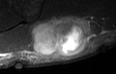
MRI of an extremity soft-tissue mass, one axial slice. Position 19 of 36 along the scan axis. STIR. MR volume resampled by the dataset authors to the PET/CT grid (not the native acquisition matrix). 3.27 mm slice thickness. 116 × 74 image matrix, field of view 113 × 72 mm. Male patient. Case-level facts recorded for this patient, not image findings: histological type: pleiomorphic leiomyosarcoma; grade: high; site of the primary tumour: left buttock.
Outlined on this slice (expert contour drawn on MRI and transferred to this co-registered scan by the dataset authors):
- gross tumour volume including surrounding oedema: box from (x=28, y=17) to (x=86, y=57) px
- gross tumour volume (mass): (x=28, y=17)–(x=85, y=57)